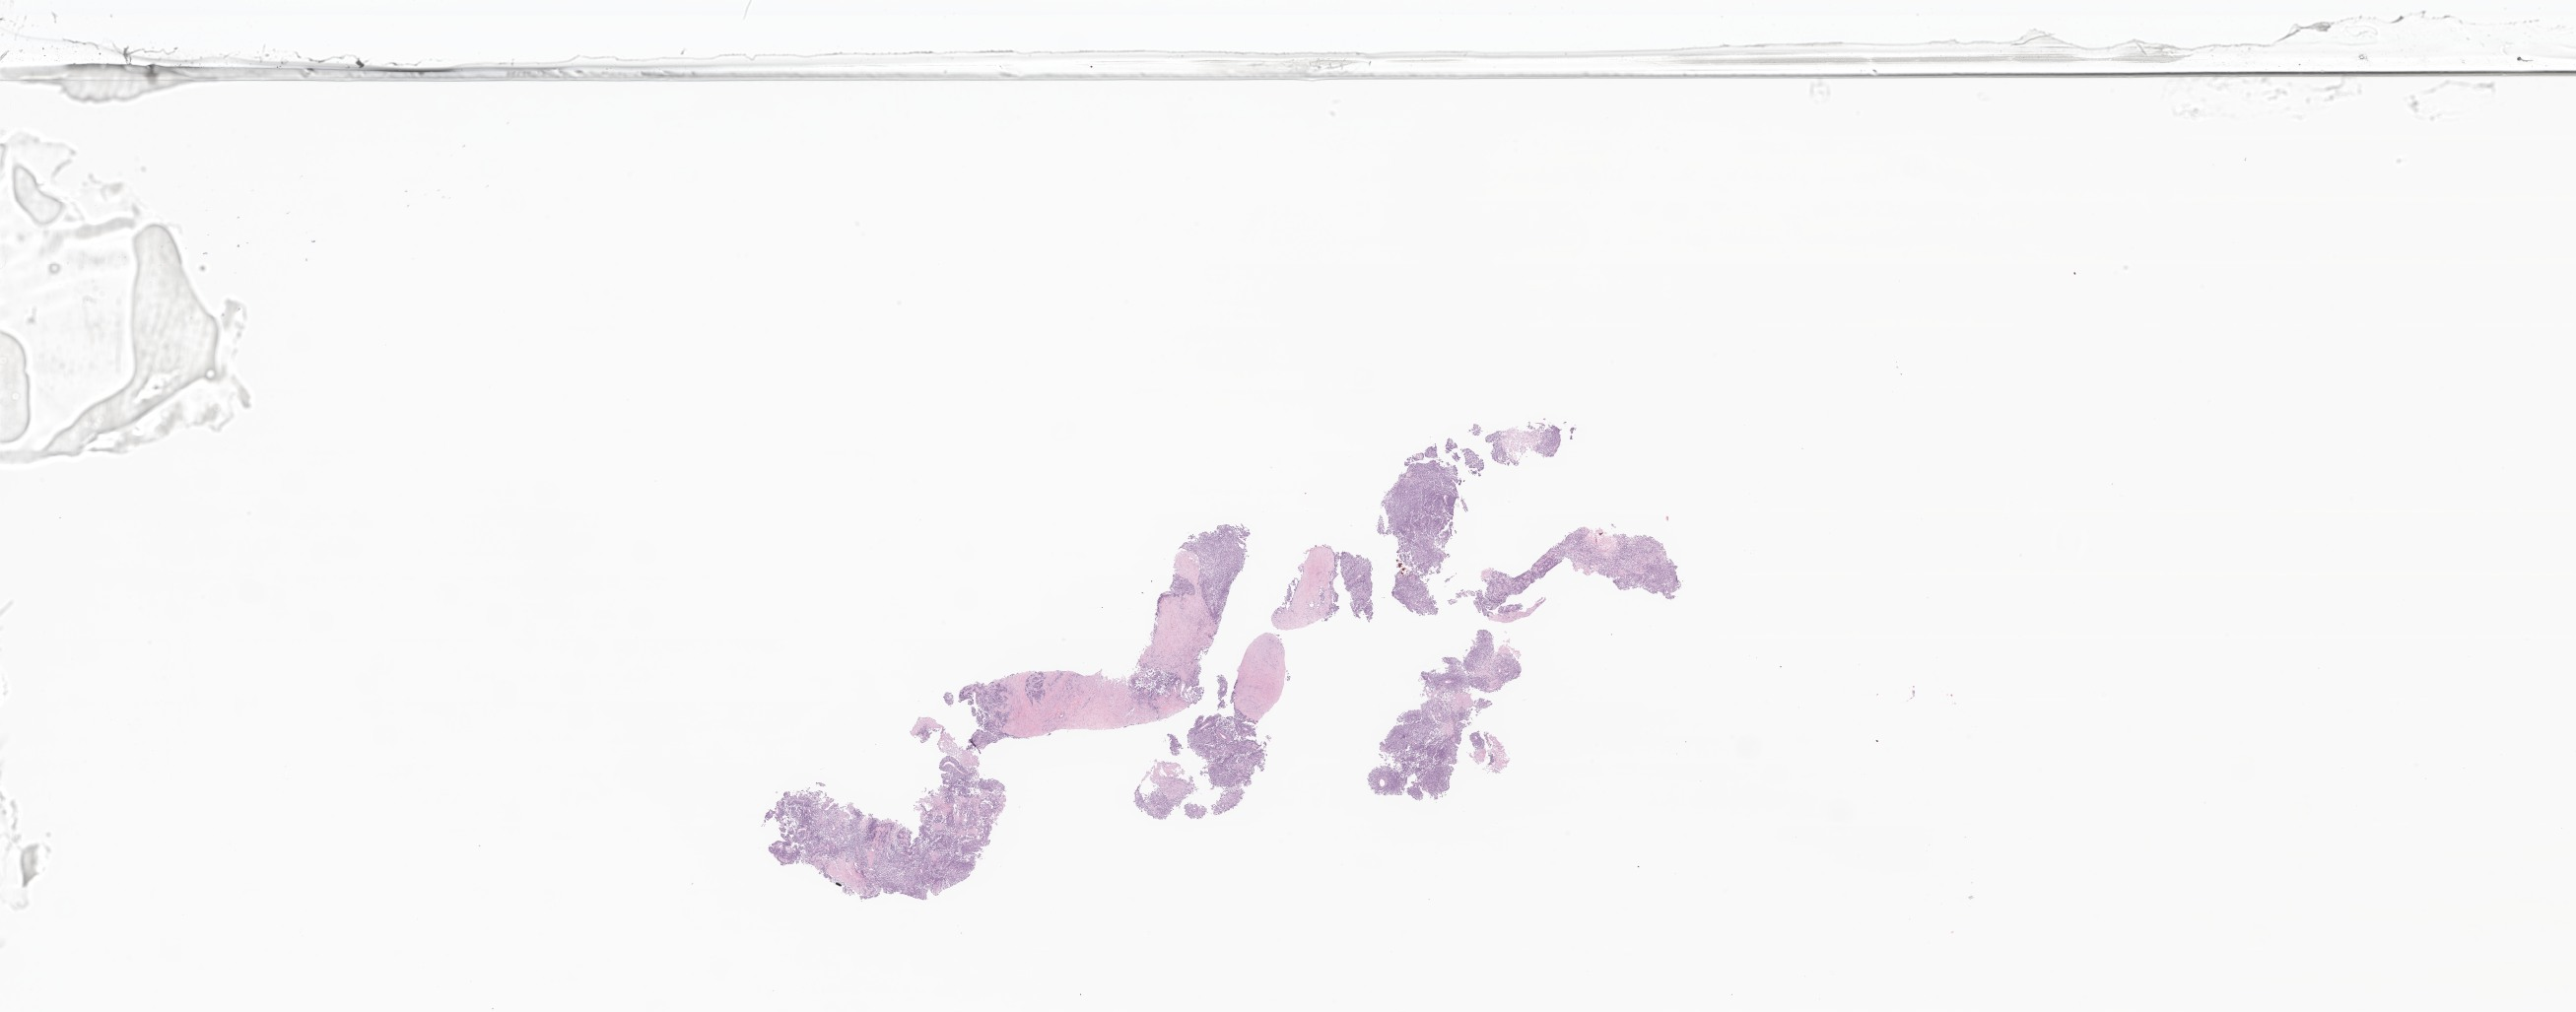
Hematoxylin and eosin (H&E) whole-slide image of tumor tissue from the pelvis — shown as a low-resolution overview of the whole scanned area (about 44.1 x 17.3 mm), formalin-fixed paraffin-embedded section. Male patient, age 108 months (9 years).
Diagnosis (ICD-O-3 morphology term): Alveolar rhabdomyosarcoma.